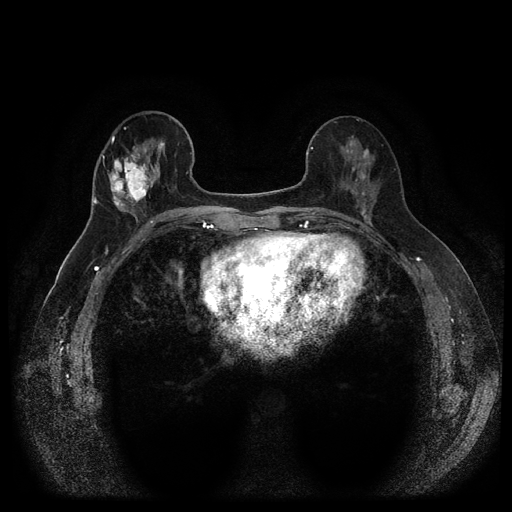
Breast MRI (dynamic contrast-enhanced, multi-phase), one axial slice. Position 42 of 116 along the scan axis. Dynamic contrast-enhanced series, time point 2 of 5 at this slice position (early post-contrast). 1.5 T. TE 2.6 ms, TR 5.4 ms. 512 × 512 image matrix, field of view 340 × 340 mm. Patient: female, 56 years.
Structures marked on this image (semi-automatically segmented with operator editing):
- breast lesion (labelled 'tumour' in the annotation; benign lesions carry a separate 'benign' label): bounding box [x1, y1, x2, y2] px = [107, 149, 156, 212]